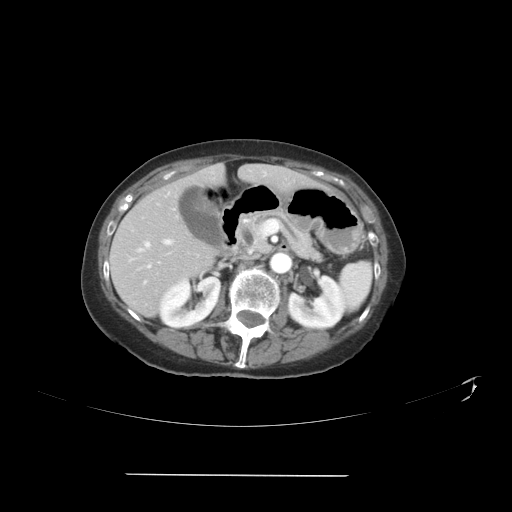
Contrast-enhanced abdominal CT, one axial slice; reconstruction kernel STANDARD; intravenous contrast given; soft-tissue window (W 400 / L 40 HU); 512 × 512 image matrix, field of view 431 × 431 mm. Female patient, age 74 years. Case-level facts recorded for this patient, not image findings: diagnosis: colorectal cancer liver metastases, imaged before liver resection; multiple liver metastases: yes.
Annotated regions visible in this slice (expert manual segmentation):
- hepatic veins: box from (x=137, y=208) to (x=175, y=268) px
- liver: (x=110, y=165)–(x=307, y=315)
- planned liver remnant (the part of the liver to remain after resection): (x=119, y=165)–(x=308, y=249)
- portal vein (with intrahepatic branches): (x=164, y=239)–(x=171, y=244)